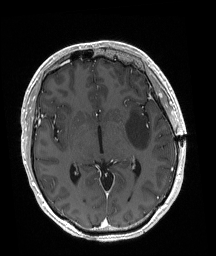
Brain MRI from a brain-tumour surgery series, one axial slice; slice 105 of 192 in the series (ordered by position); T1-weighted post-contrast; 1 mm slice thickness; 216 × 256 image matrix. Case-level facts recorded for this patient, not image findings: histopathology: Astrocytoma; WHO grade: 3; IDH mutation: yes.
Outlined on this slice (manually delineated by an expert):
- tumour: box from (x=126, y=109) to (x=151, y=149) px